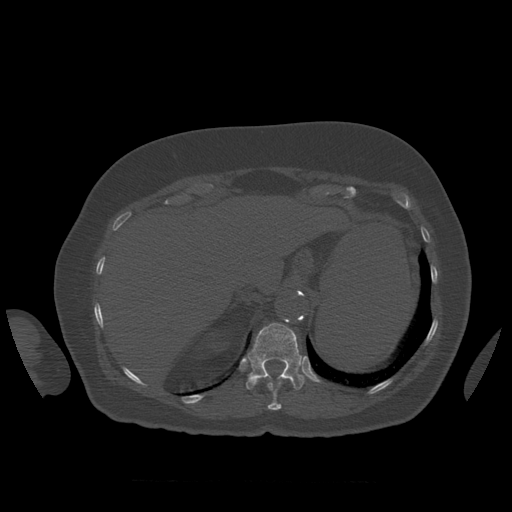
CT including the spine, one axial slice. Position 307 of 399 along the scan axis. 120 kVp. Bone window (W 1800 / L 400 HU). 1.25 mm slice thickness. 512 × 512 image matrix, field of view 404 × 404 mm. Patient age 81 years. Case-level facts recorded for this patient, not image findings: primary cancer: renal; vertebrae with lytic lesions (as recorded): L1.
Structures marked on this image (semi-automatic segmentation, software-assisted and operator-edited):
- T11 vertebra: bounding box [x1, y1, x2, y2] px = [268, 383, 282, 410]
- T12 vertebra: [246, 323, 305, 391]